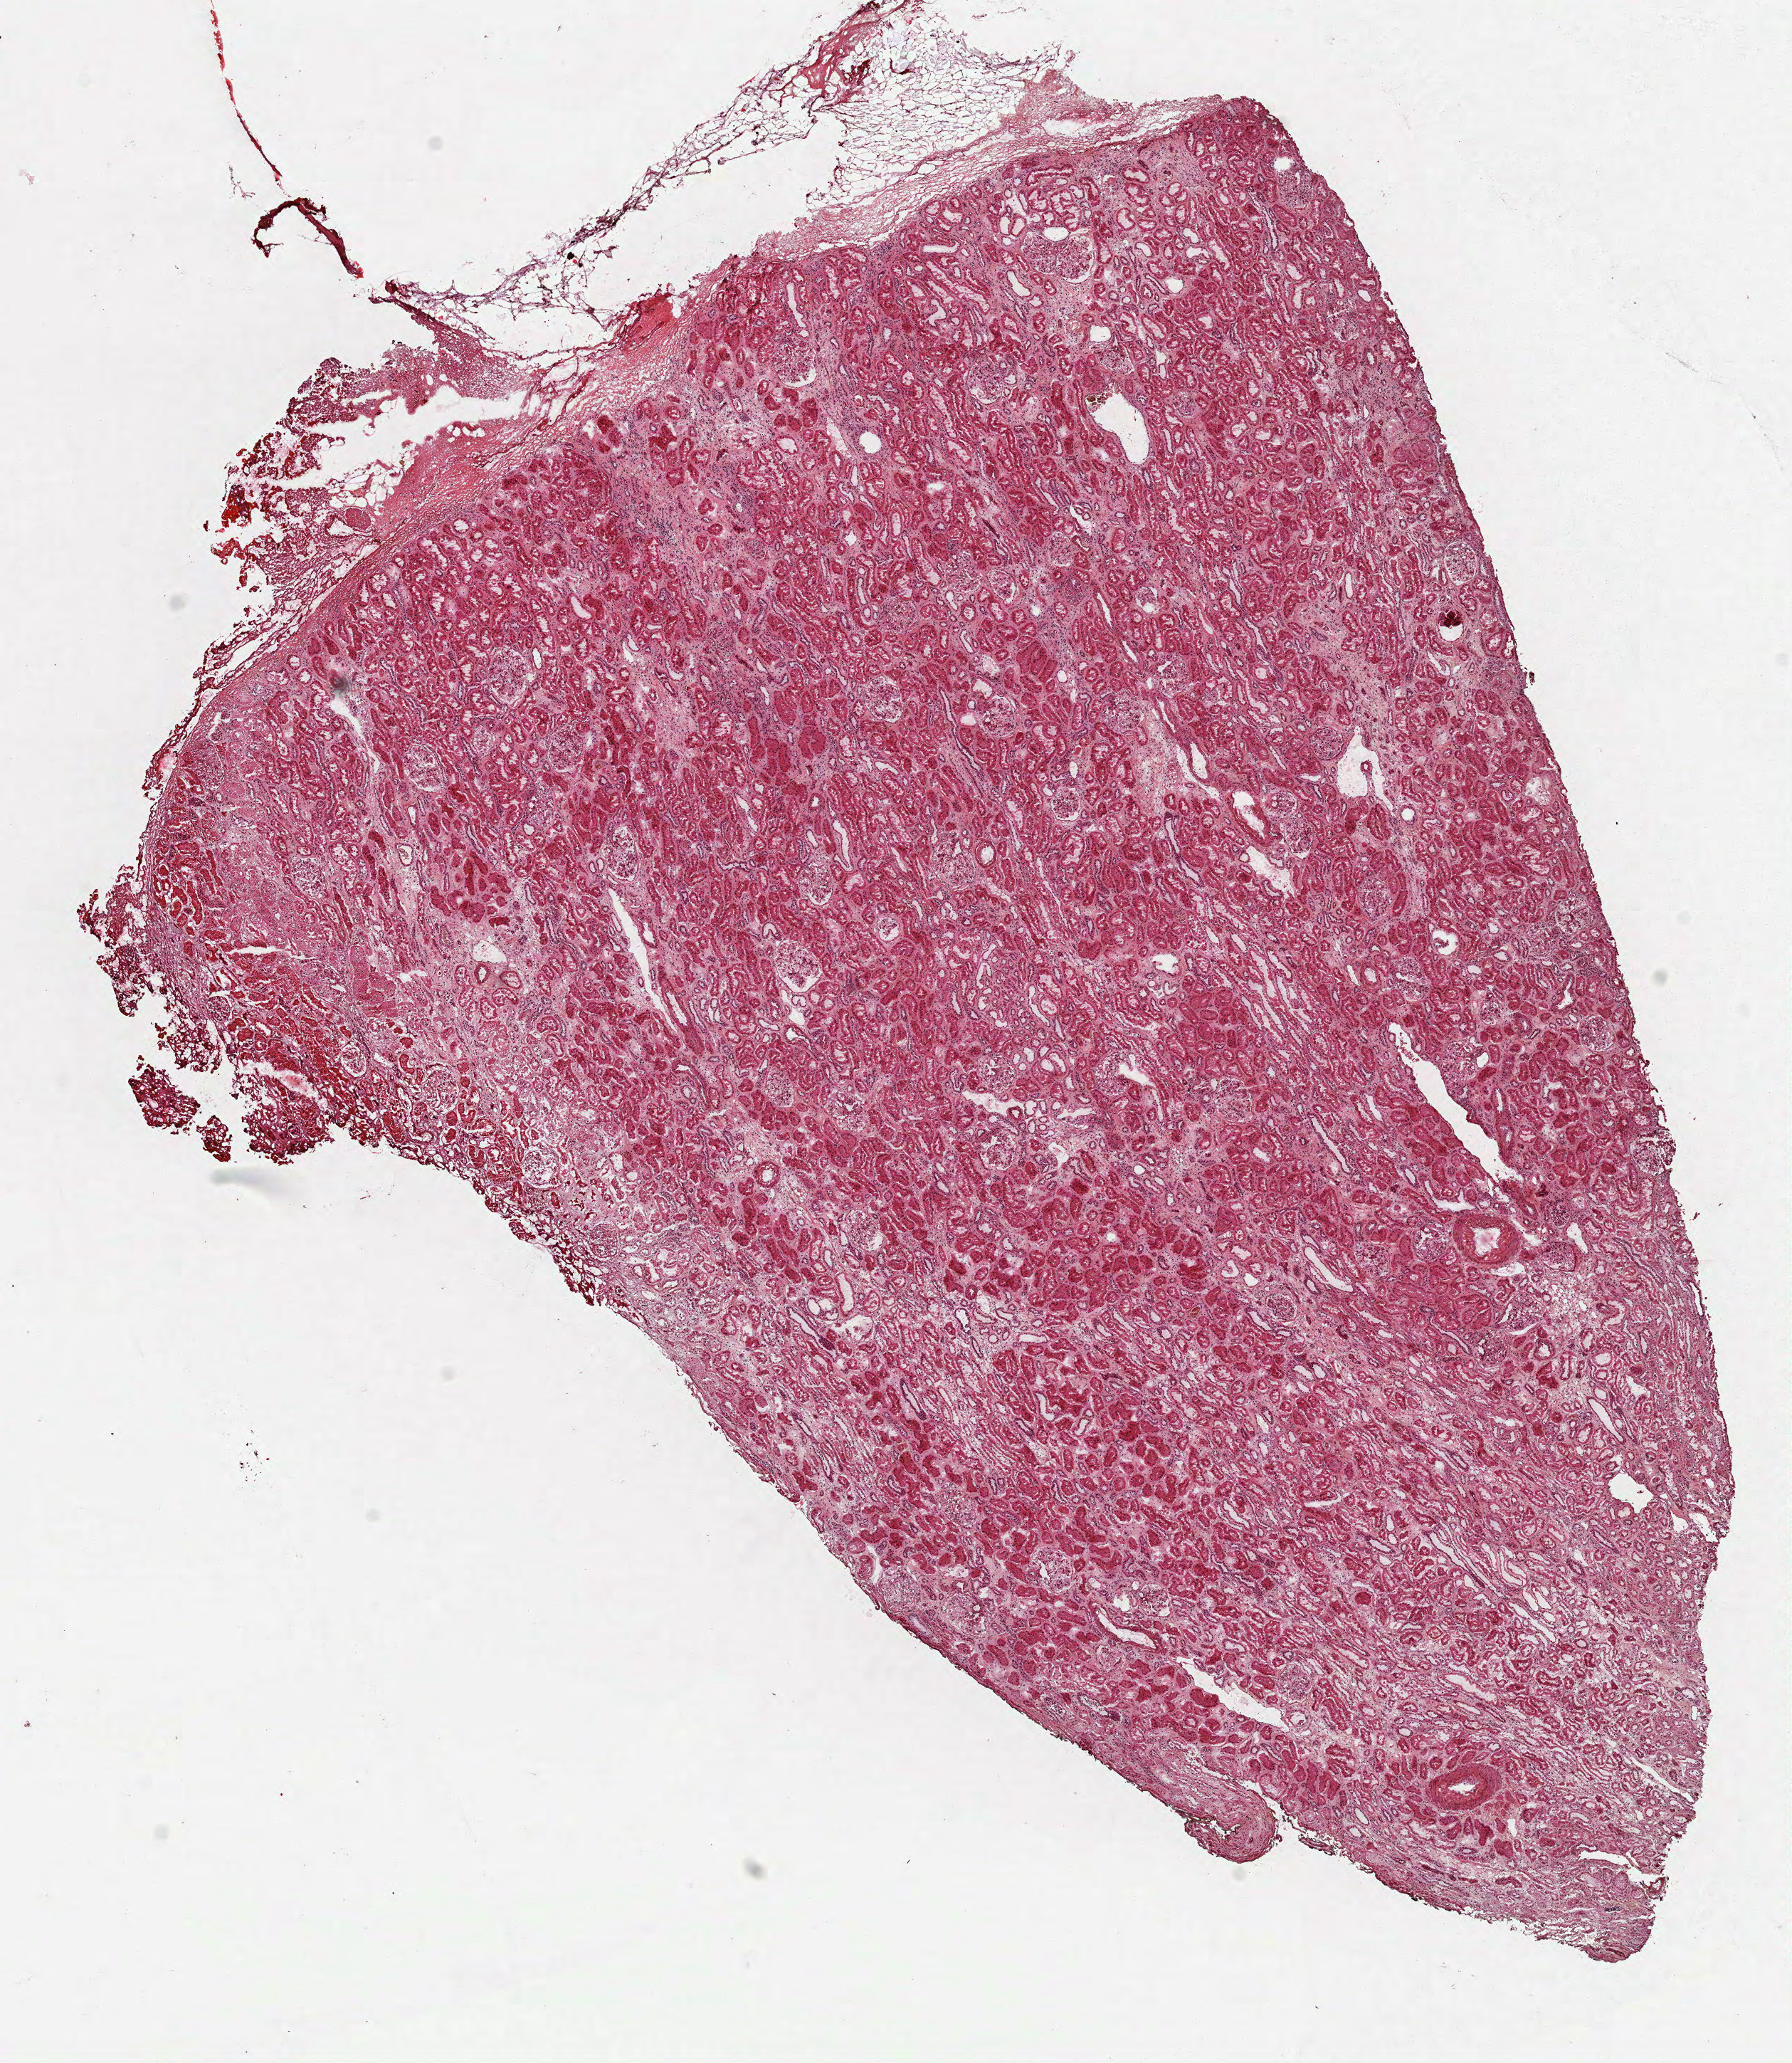
Digitized Hematoxylin and eosin (H&E) stained tissue section (whole slide), shown as a low-resolution overview of the whole scanned area (about 10.2 x 11.7 mm, slide scanned at 40x), frozen section from the top of the tissue portion, solid tissue normal (non-tumour tissue) sample from the kidney. Male patient; age at initial diagnosis 71 years.
This section: solid tissue normal sample (biorepository sample class). Patient diagnosis: Papillary adenocarcinoma, NOS.